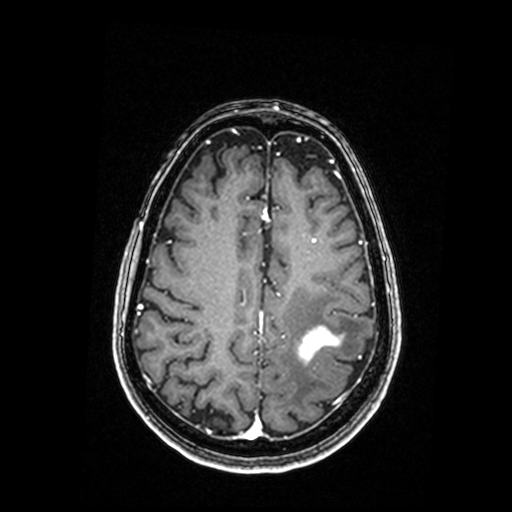
Brain MRI from a brain-tumour surgery series, one axial slice; position 62 of 192 along the scan axis; T1-weighted post-contrast; 0.98 mm slice thickness; 512 × 512 image matrix. Case-level facts recorded for this patient, not image findings: histopathology: Metastastic Carcinoma, Poorly Differentiated.
Annotated regions visible in this slice (outlined manually by an expert reader):
- tumour: bounding box <296,327,341,363> (left, top, right, bottom; pixels)